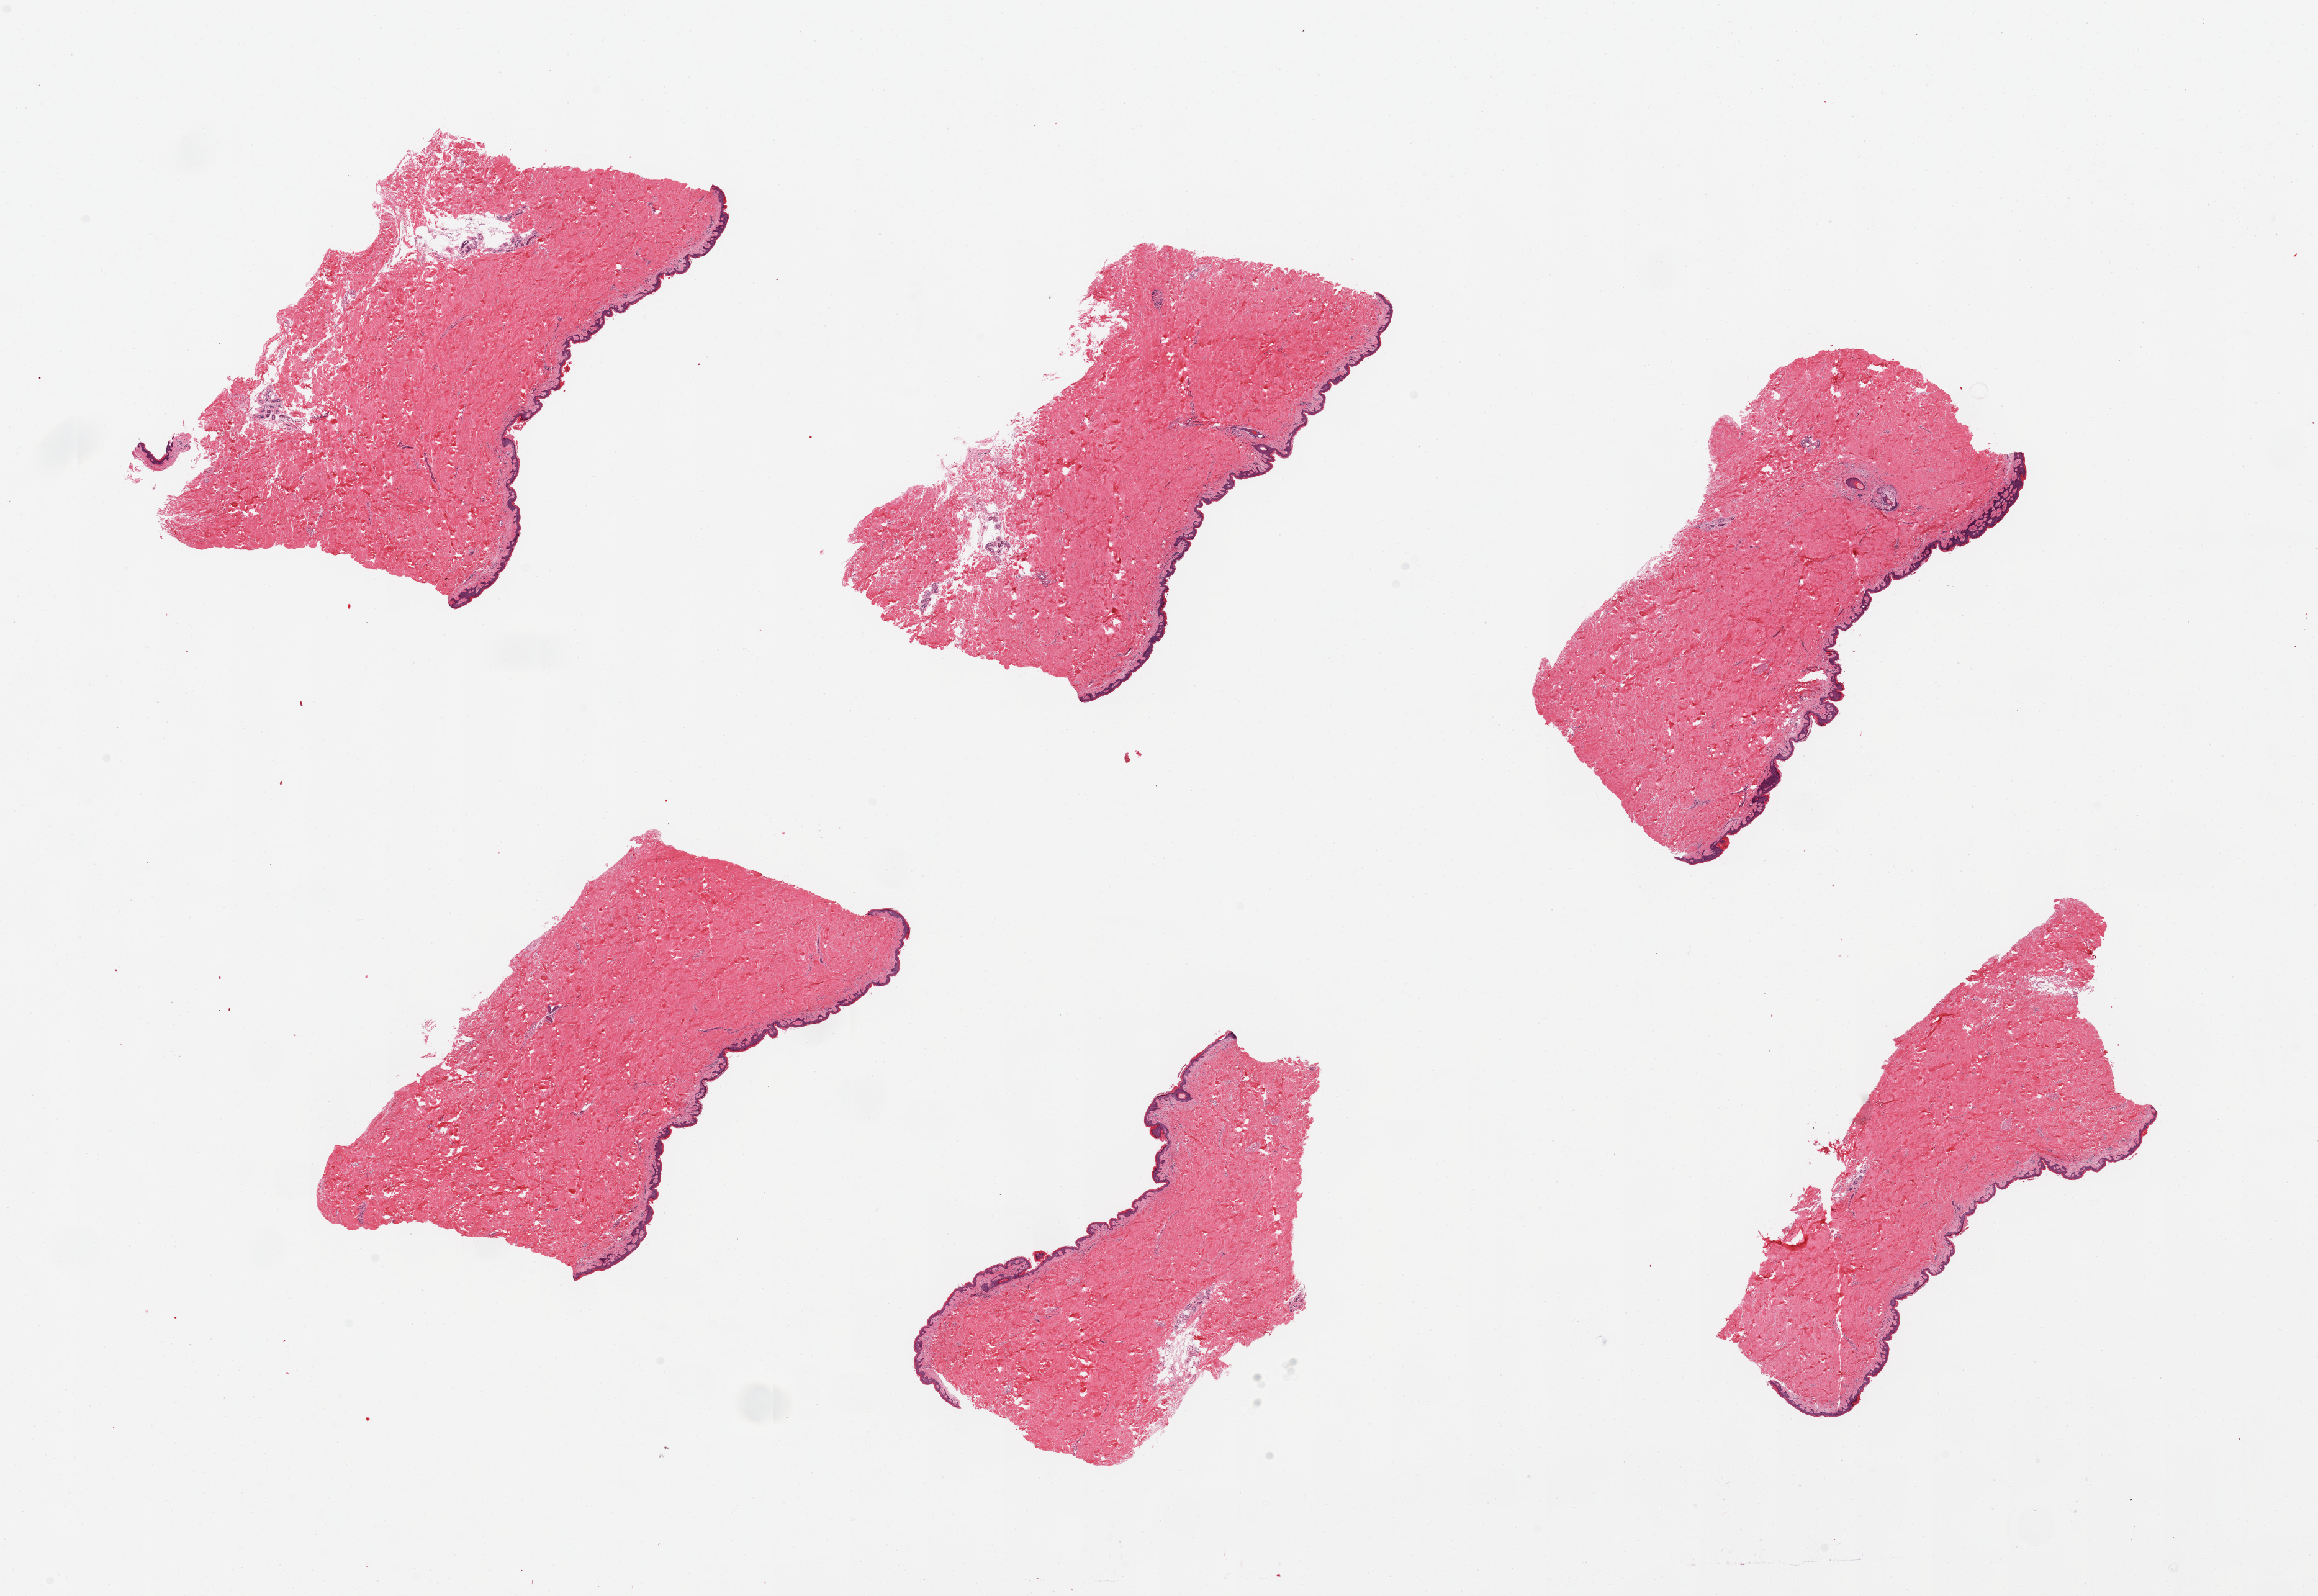
Digitized hematoxylin and eosin (H&E)-stained section, whole scanned area (about 29.5 x 20.3 mm, slide scanned at 20x) shown as a low-resolution overview. PAXgene-fixed paraffin-embedded (PFPE) section. Target tissue: skin of suprapubic region. Donor tissue sample. Donor: male.
* pathologist's review note for this sample: 6 pieces, minimal dermal fat, squamous epithelium is ~50 microns